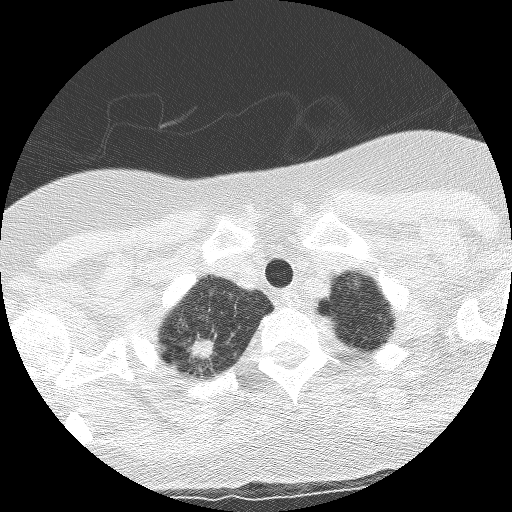
Low-dose screening chest CT, axial slice. Third screening round (two years after baseline). Lung window (W 1500 / L -600 HU). Slice 12 of 130 in the series. Female participant, aged 56 years at enrolment. Current smoker at enrolment.
- Expert-annotated lung lesion, bounding box <168,329,224,378> (left, top, right, bottom; pixels).
- Reader record for this screening exam (exam-level; its link to the box is not recorded): non-calcified nodule or mass ≥4 mm, right upper lobe, 17 × 10 mm, spiculated (stellate) margins, mixed attenuation, pre-existing on the prior screen: yes; interval growth: yes.
- Lung cancer was diagnosed 24 days after this screen: large cell carcinoma, NOS, right upper lobe, poorly differentiated (G3), stage IB (AJCC 6th edition), 15 mm at pathology.